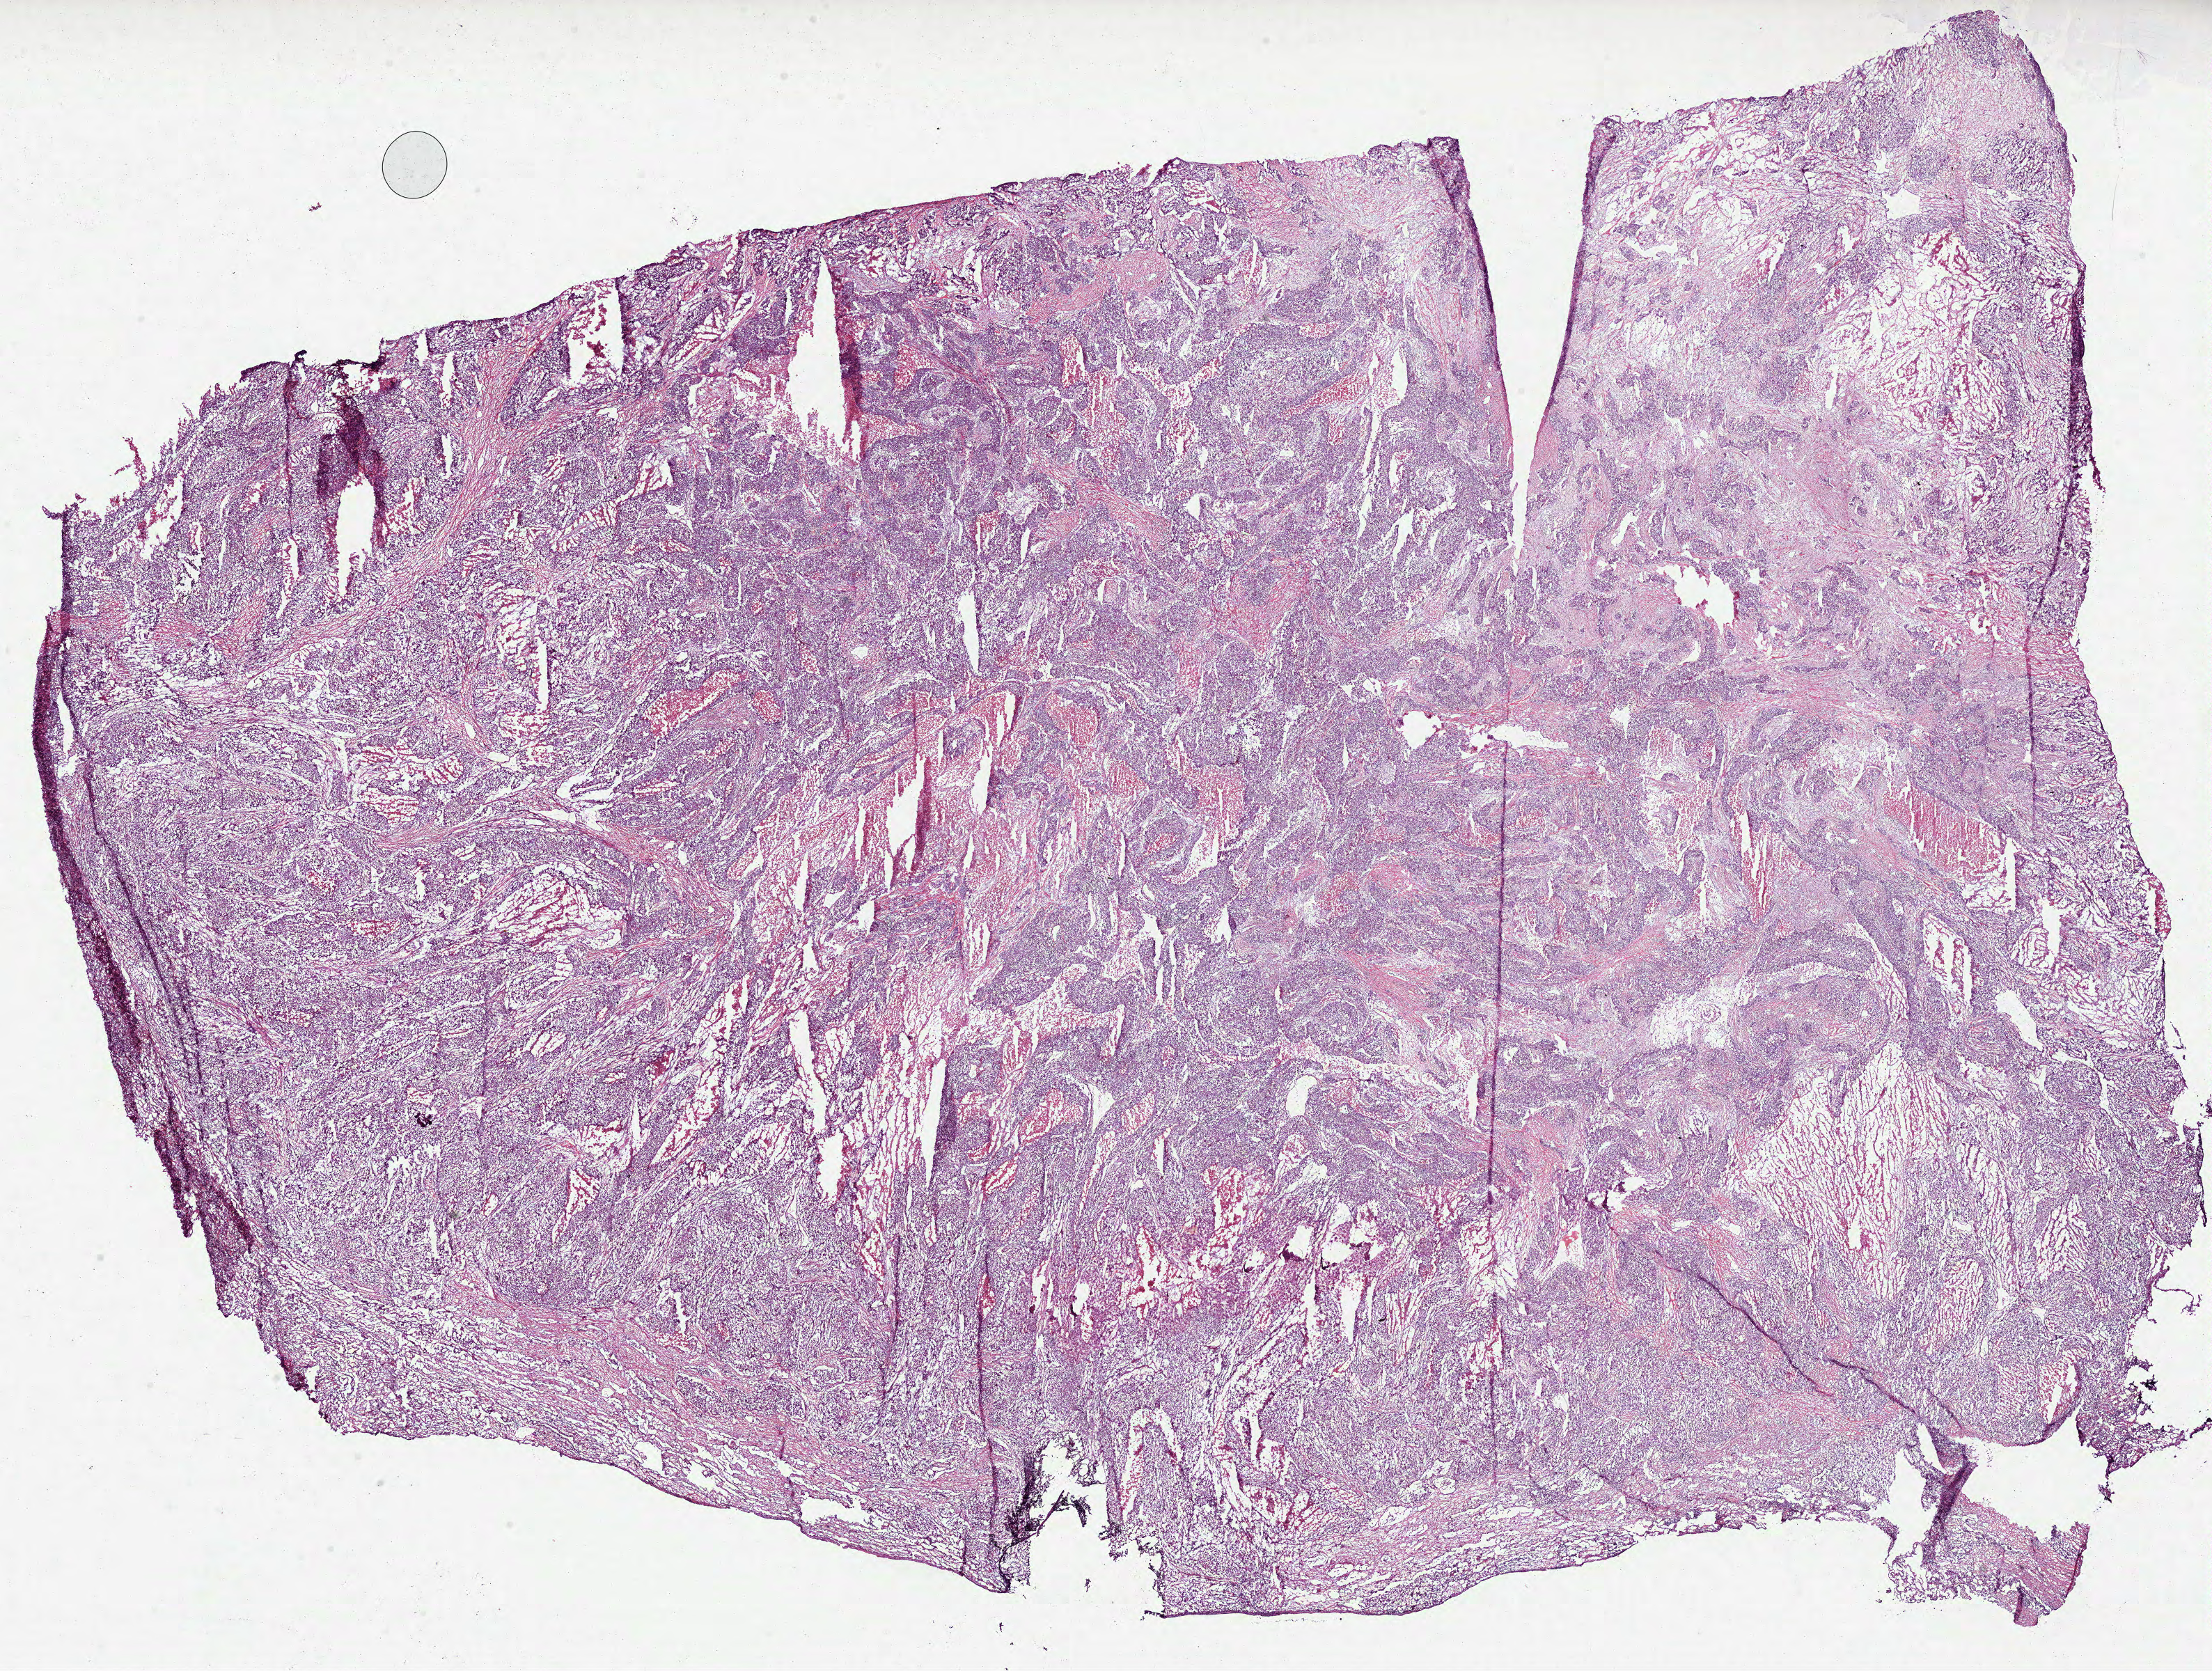
H&E-stained whole-slide image — low-resolution overview of the scanned area, about 25.6 x 19.4 mm, frozen section from the top of the tissue portion, lung, primary tumour sample. Male, age 46 years at initial diagnosis. Pathologist review of this section (percent, as recorded): tumour cells 70%, tumour nuclei 75%, normal cells 0%, stromal cells 10%, necrosis 20%.
Pathologic diagnosis: Squamous cell carcinoma, NOS (upper lobe, lung). AJCC pathologic stage: IB (7th edition).